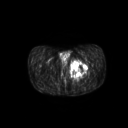
FDG PET of an extremity soft-tissue mass (from a PET/CT study), one axial slice. Slice 37 of 267 in the series (ordered by position). 3.27 mm slice thickness. 128 × 128 image matrix, field of view 600 × 600 mm. Male patient, age 59 years. Case-level facts recorded for this patient, not image findings: histological type: pleiomorphic liposarcoma; grade: high; site of the primary tumour: left thigh.
Annotated regions visible in this slice (expert contour drawn on MRI and transferred to this co-registered scan by the dataset authors):
- gross tumour volume including surrounding oedema: box from (x=69, y=59) to (x=87, y=79) px
- gross tumour volume (mass): (x=70, y=60)–(x=87, y=77)